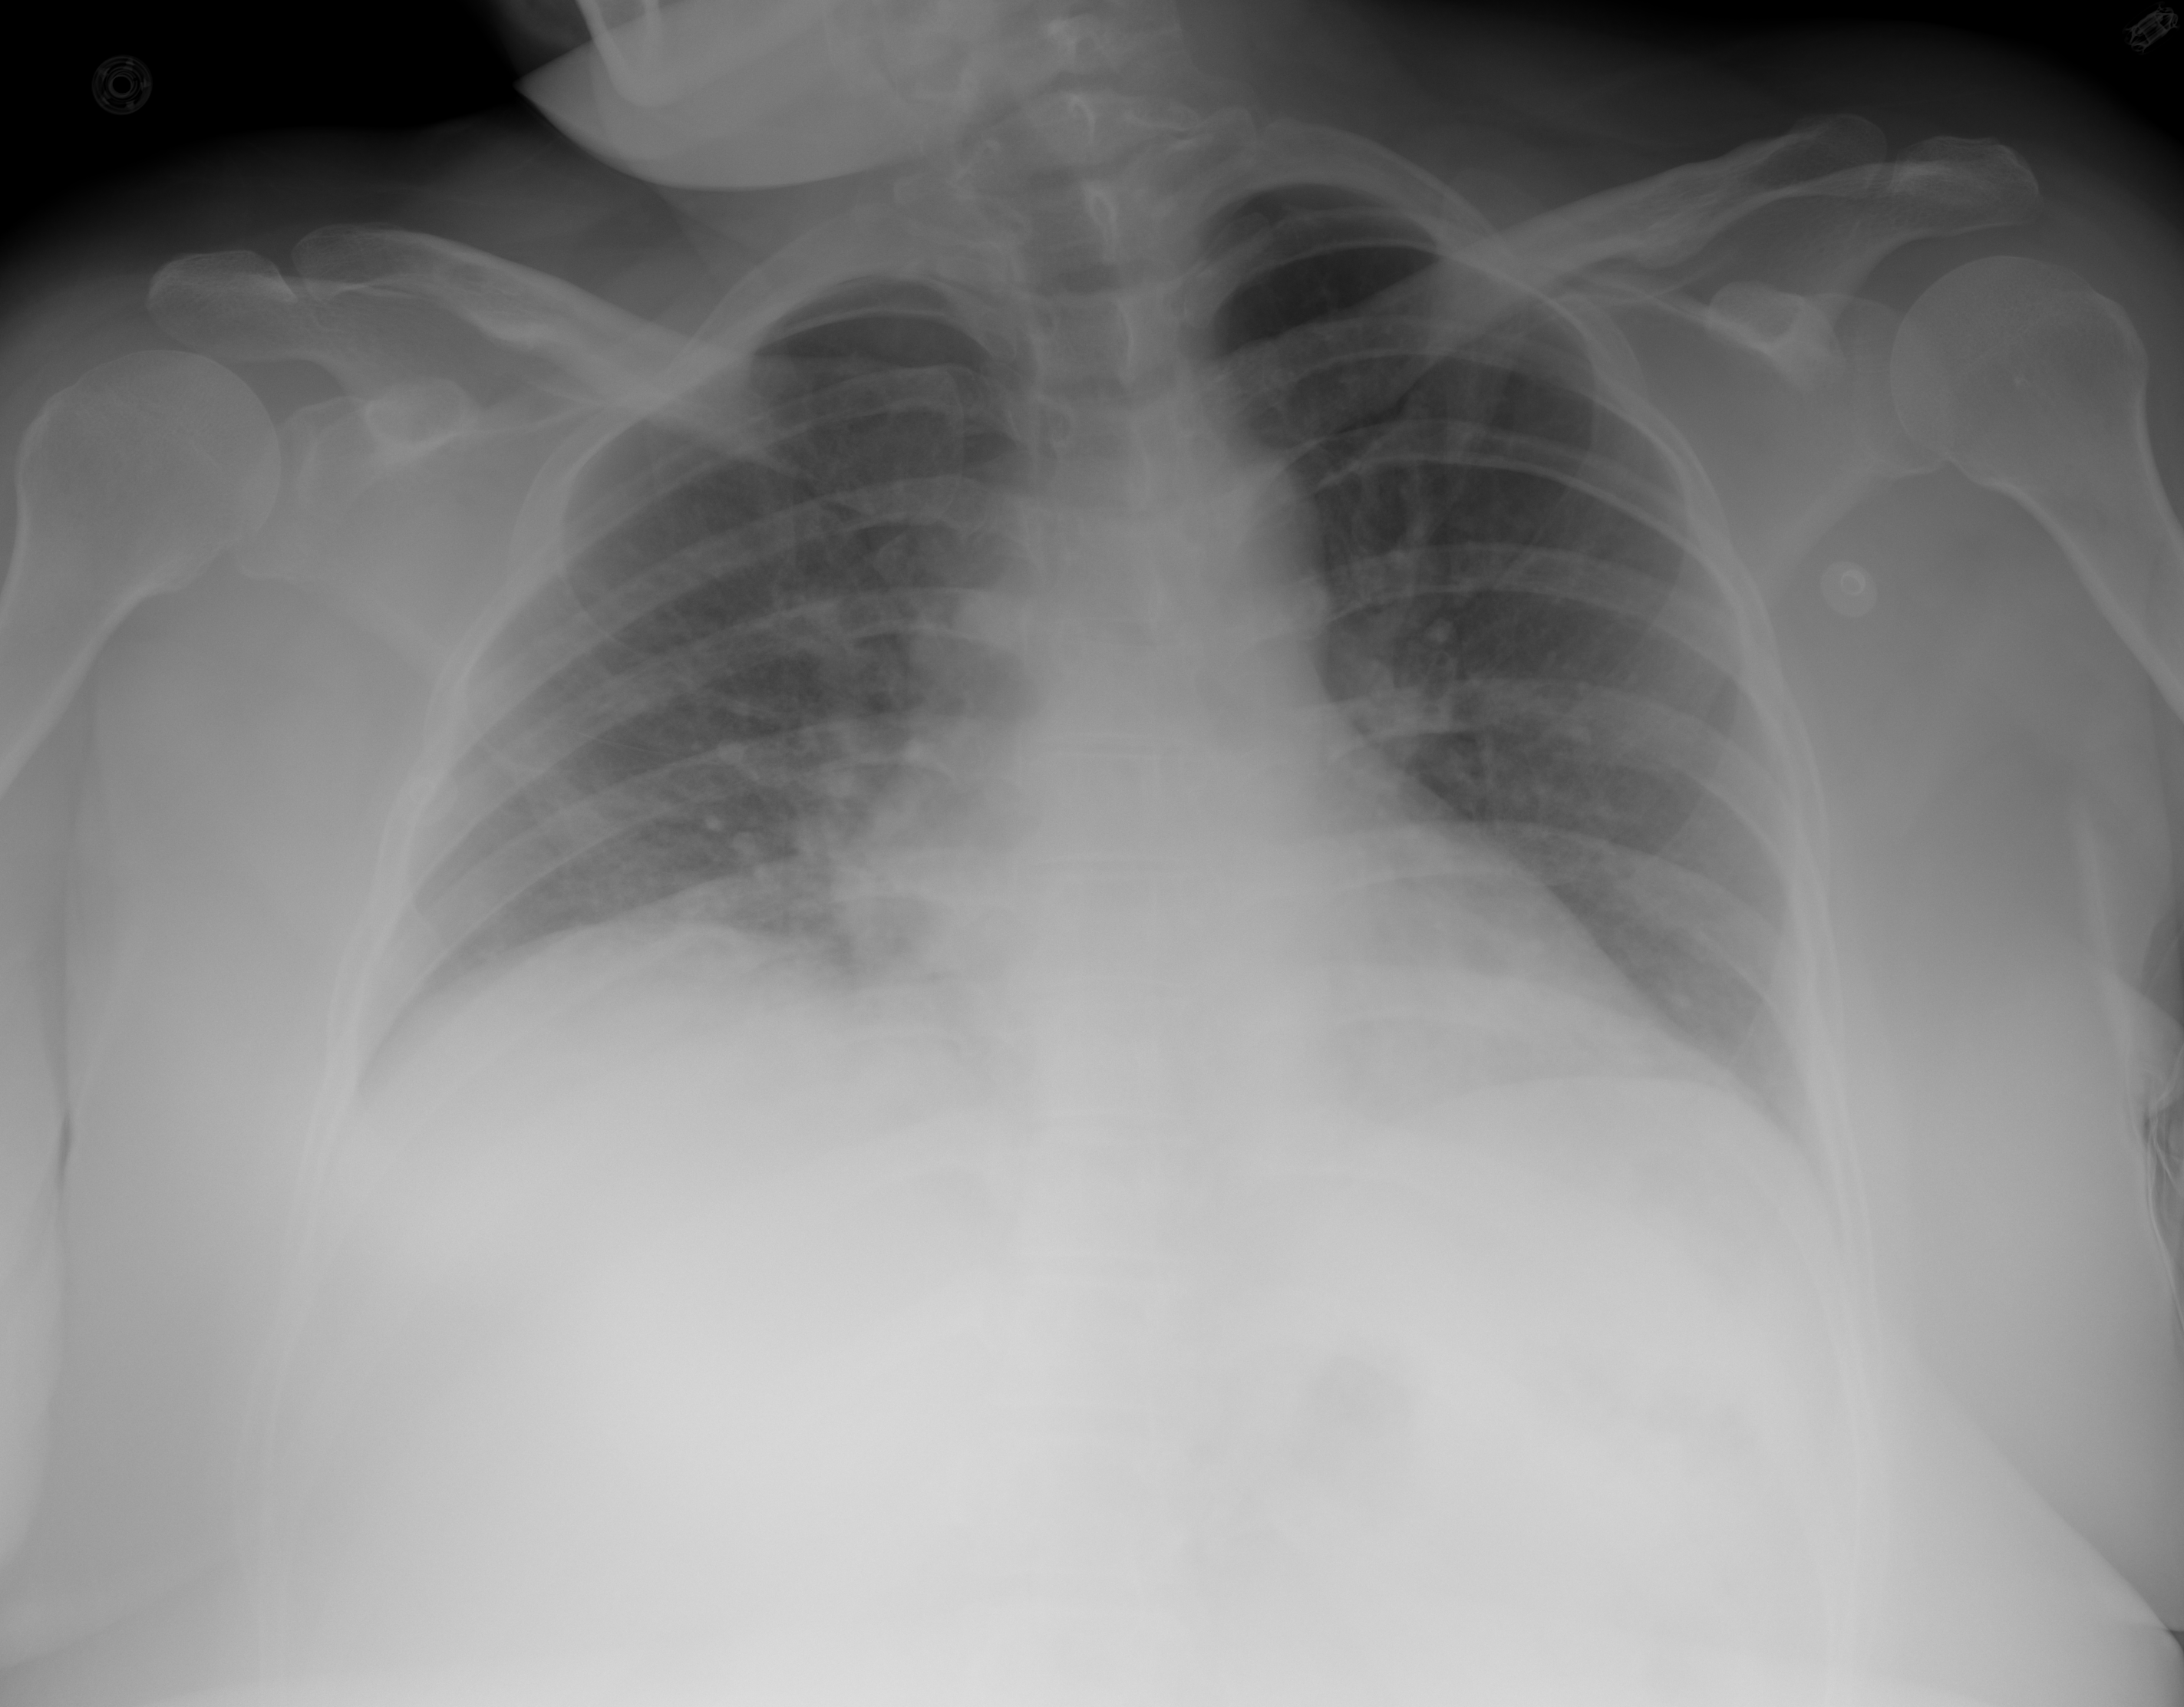
Portable chest radiograph, AP projection. Female patient, age 35 years; imaged 8 days after the COVID-19 diagnosis.
Radiologist key findings (as recorded): The lungs are hypoinflated with bibasilar airspace opacities.